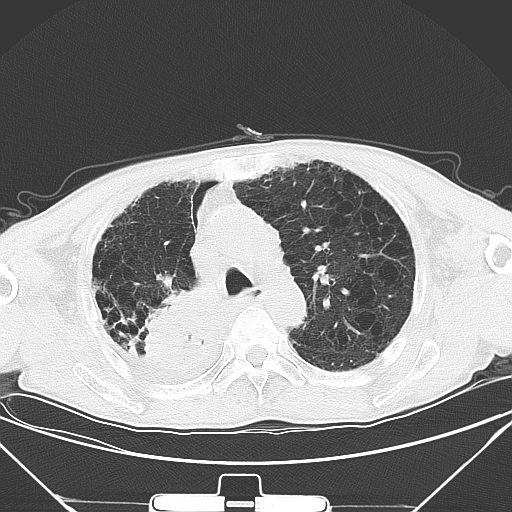
Chest CT, one axial slice; position 34 of 50 along the scan axis; lung window (W 1500 / L -600 HU); 5 mm slice thickness; 512 × 512 image matrix, field of view 373 × 373 mm. Patient: male, 65 years. Case-level facts recorded for this patient, not image findings: clinical TNM (as recorded): T3 N1 M1a.
Annotated regions visible in this slice (bounding box drawn by a radiologist):
- lung tumour (recorded histology: squamous cell carcinoma): bounding box <137,292,222,363> (left, top, right, bottom; pixels)